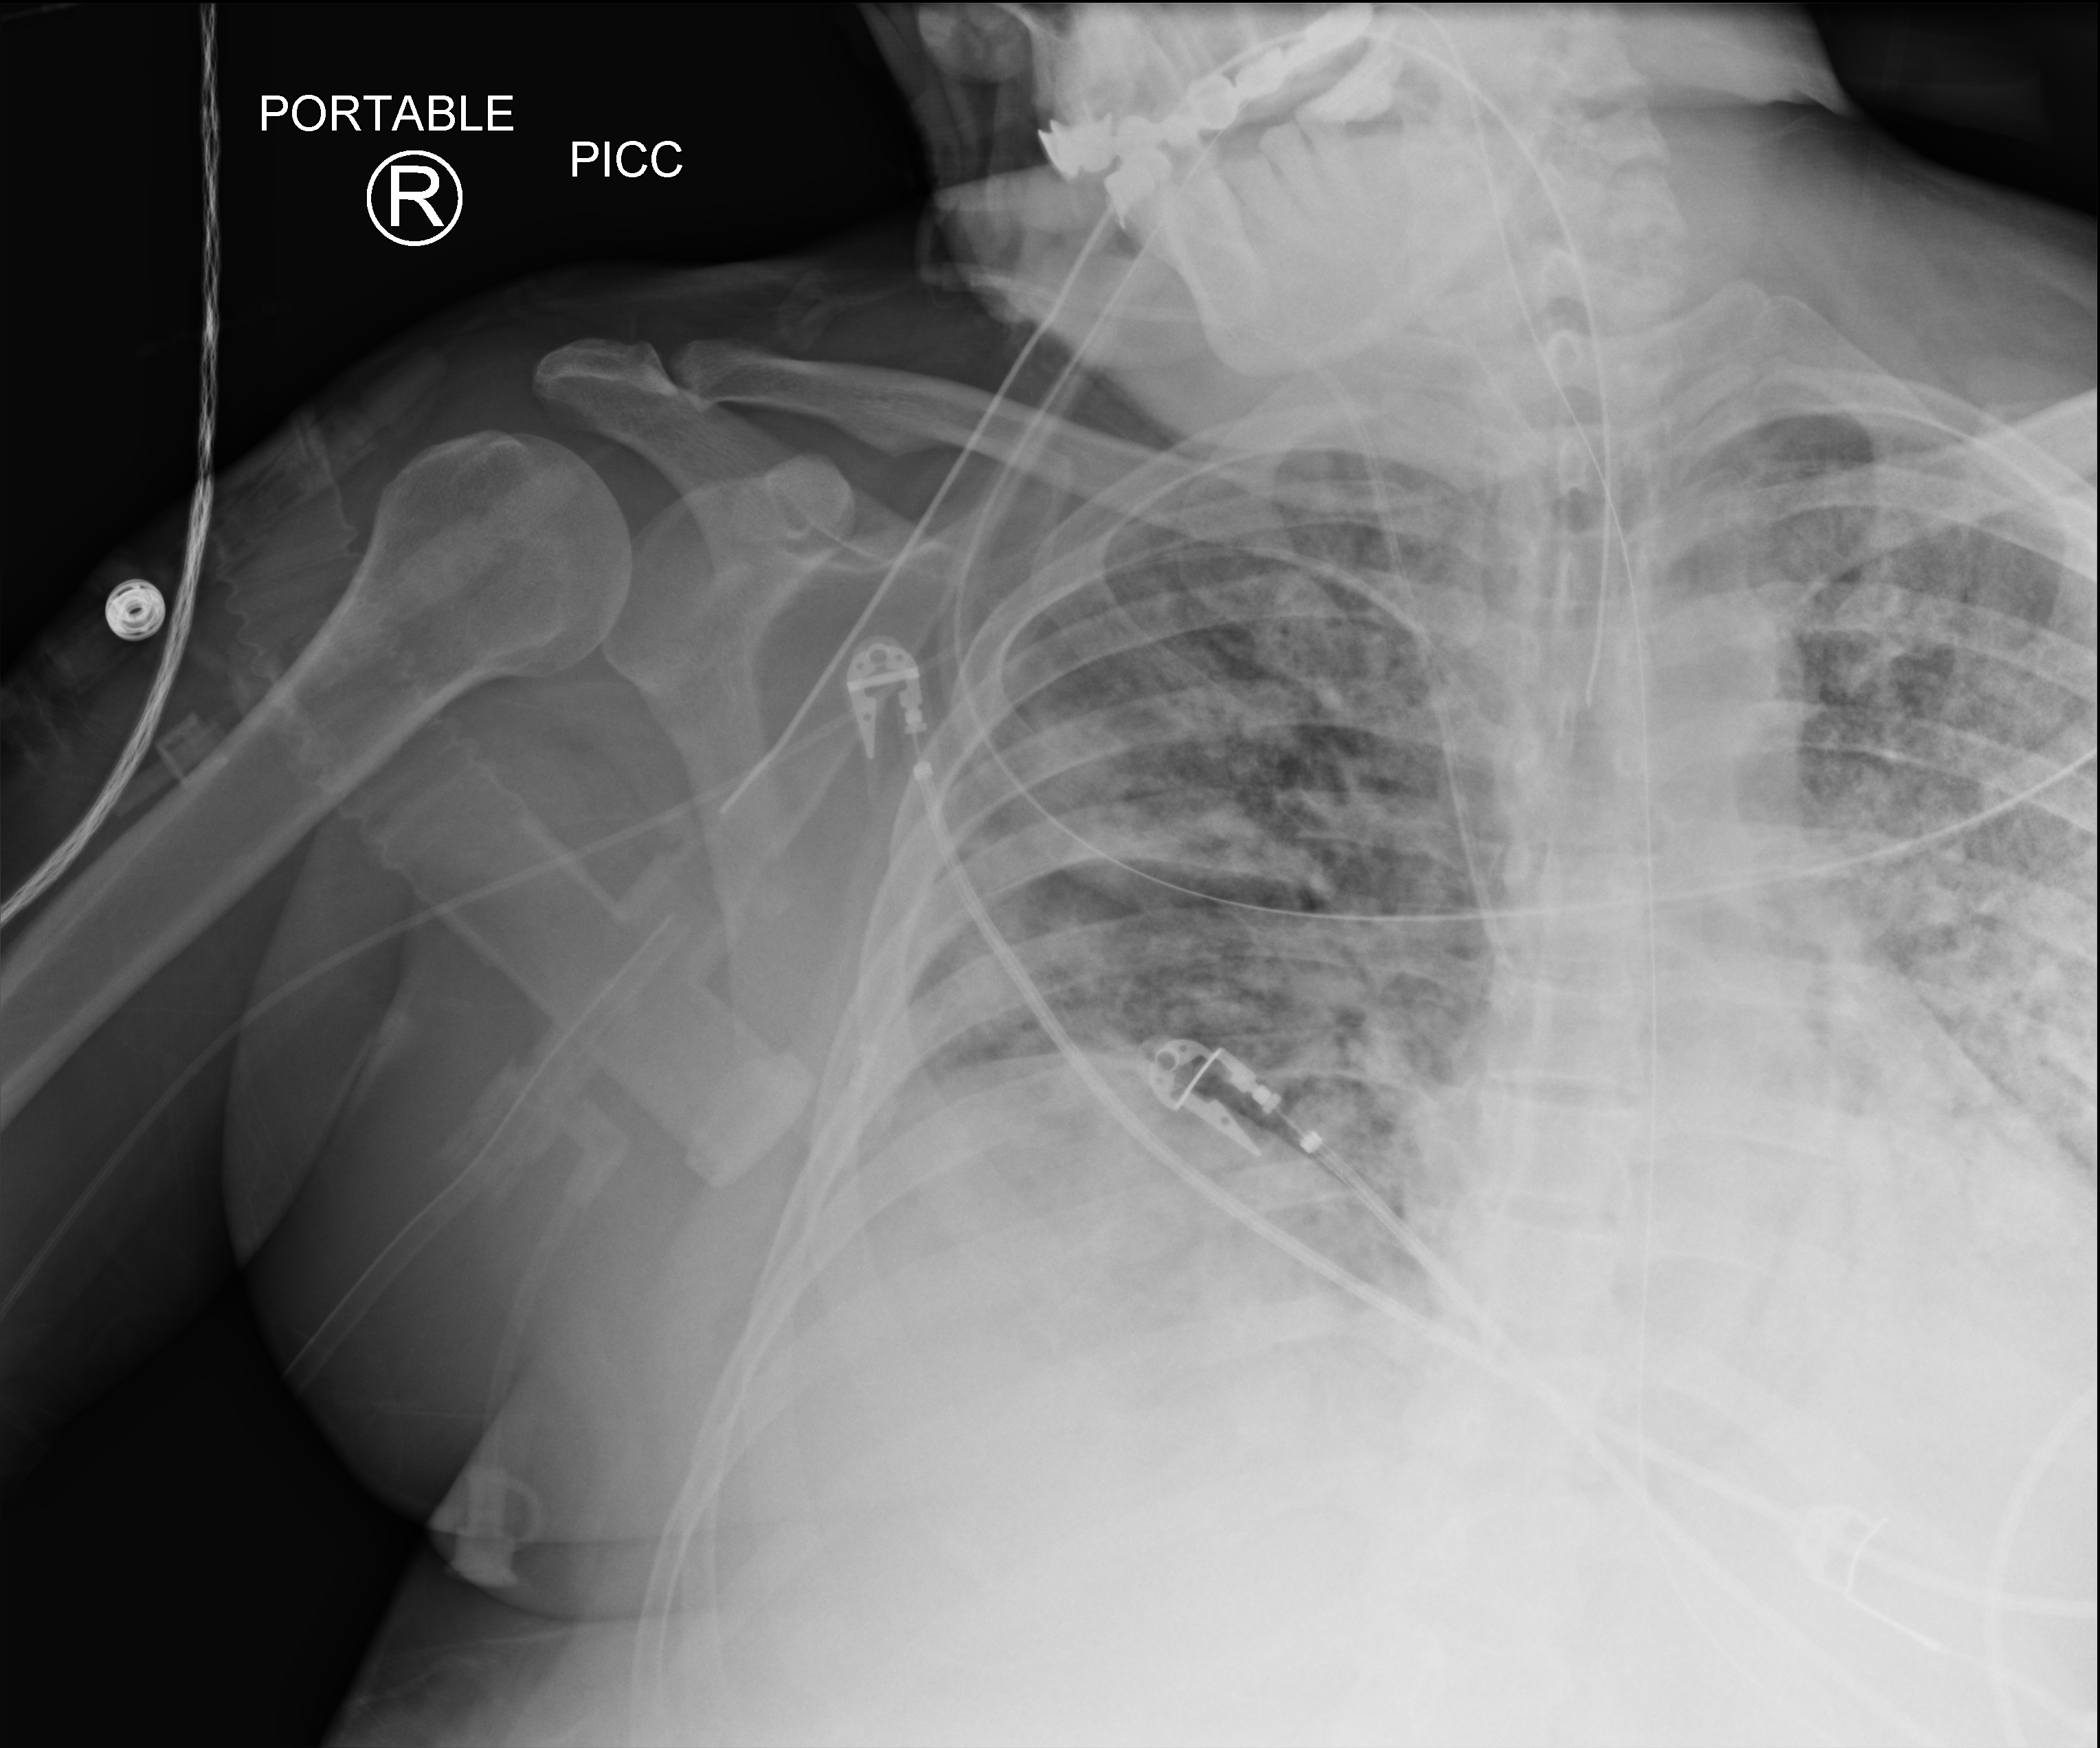
Chest X-ray (portable); anteroposterior (AP) projection. Male patient hospitalised with COVID-19, age 18–59 years.
Hospital-stay facts (about this admission, not read from this image; timing relative to this image not recorded): smoking status (admission record): never.